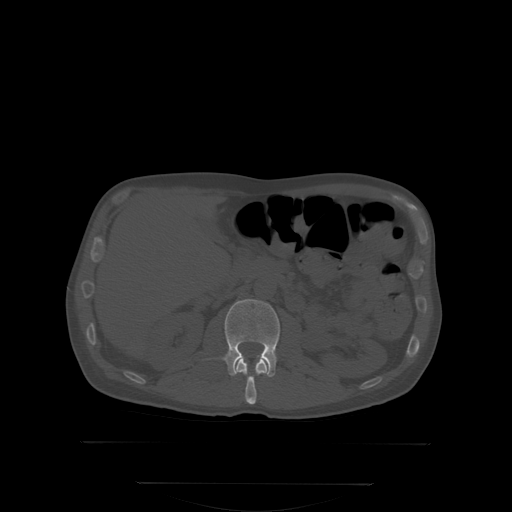
CT including the spine, one axial slice. Slice 143 of 350 in the series (ordered by position). Bone window (W 1800 / L 400 HU). 2.5 mm slice thickness. 512 × 512 image matrix, field of view 500 × 500 mm. Patient: male, 58 years. Case-level facts recorded for this patient, not image findings: primary cancer: prostate; vertebrae with lytic lesions (as recorded): L1.
Outlined on this slice (semi-automatic segmentation, software-assisted and operator-edited):
- L1 vertebra: box from (x=236, y=358) to (x=269, y=404) px
- L2 vertebra: (x=224, y=299)–(x=281, y=375)